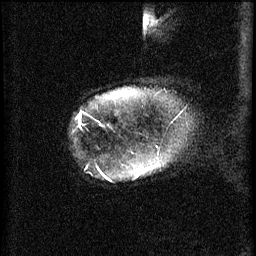
Breast MRI (dynamic contrast-enhanced), one sagittal slice. Position 56 of 60 along the scan axis. 3 images stored at this slice position (order not interpretable as contrast timing). 1.5 T. TE 4.2 ms, TR 11 ms. 2 mm slice thickness. 256 × 256 image matrix. Patient: female, 44 years.
Structures marked on this image (semi-automatically segmented with operator editing):
- analysis volume of interest (the breast-tissue region the enhancement analysis was run in; not a lesion): bounding box (x1, y1, x2, y2) in pixels: (110, 152, 165, 179)
- tumour enhancement mask (voxels above the 70 % enhancement threshold inside the analysis volume of interest): (138, 166, 157, 175)